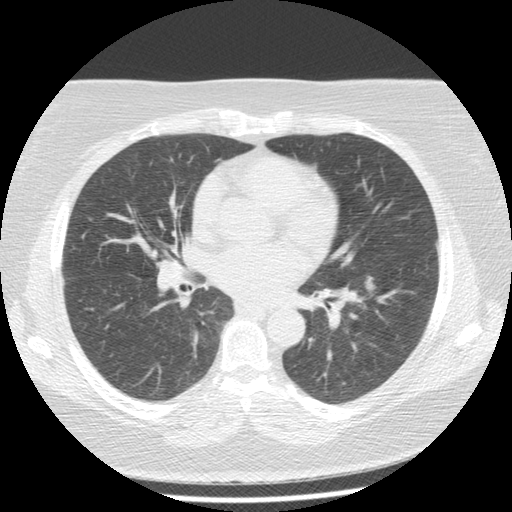
Axial slice from a low-dose chest CT screening exam, second screening round (one year after baseline), lung window (W 1500 / L -600 HU), standard (soft-tissue) reconstruction kernel (STANDARD), 120 kVp, slice 75 of 157 in the series. Female, age 65 years at enrolment. Current smoker at enrolment.
- Expert reader's lesion annotation, bounding box <352,272,382,301> (left, top, right, bottom; pixels).
- Screening reader's record for this exam (one nodule recorded; not confirmed to be the boxed lesion): non-calcified nodule or mass ≥4 mm, left lower lobe, 9 × 7 mm, poorly defined margins, soft tissue attenuation, pre-existing on the prior screen: yes; interval growth: yes.
- Official screen result: positive, other.
- Later outcome: lung cancer diagnosed 651 days after this screen — adenocarcinoma, NOS, left lower lobe, moderately differentiated (G2), stage IA (AJCC 6th edition), 12 mm at pathology.